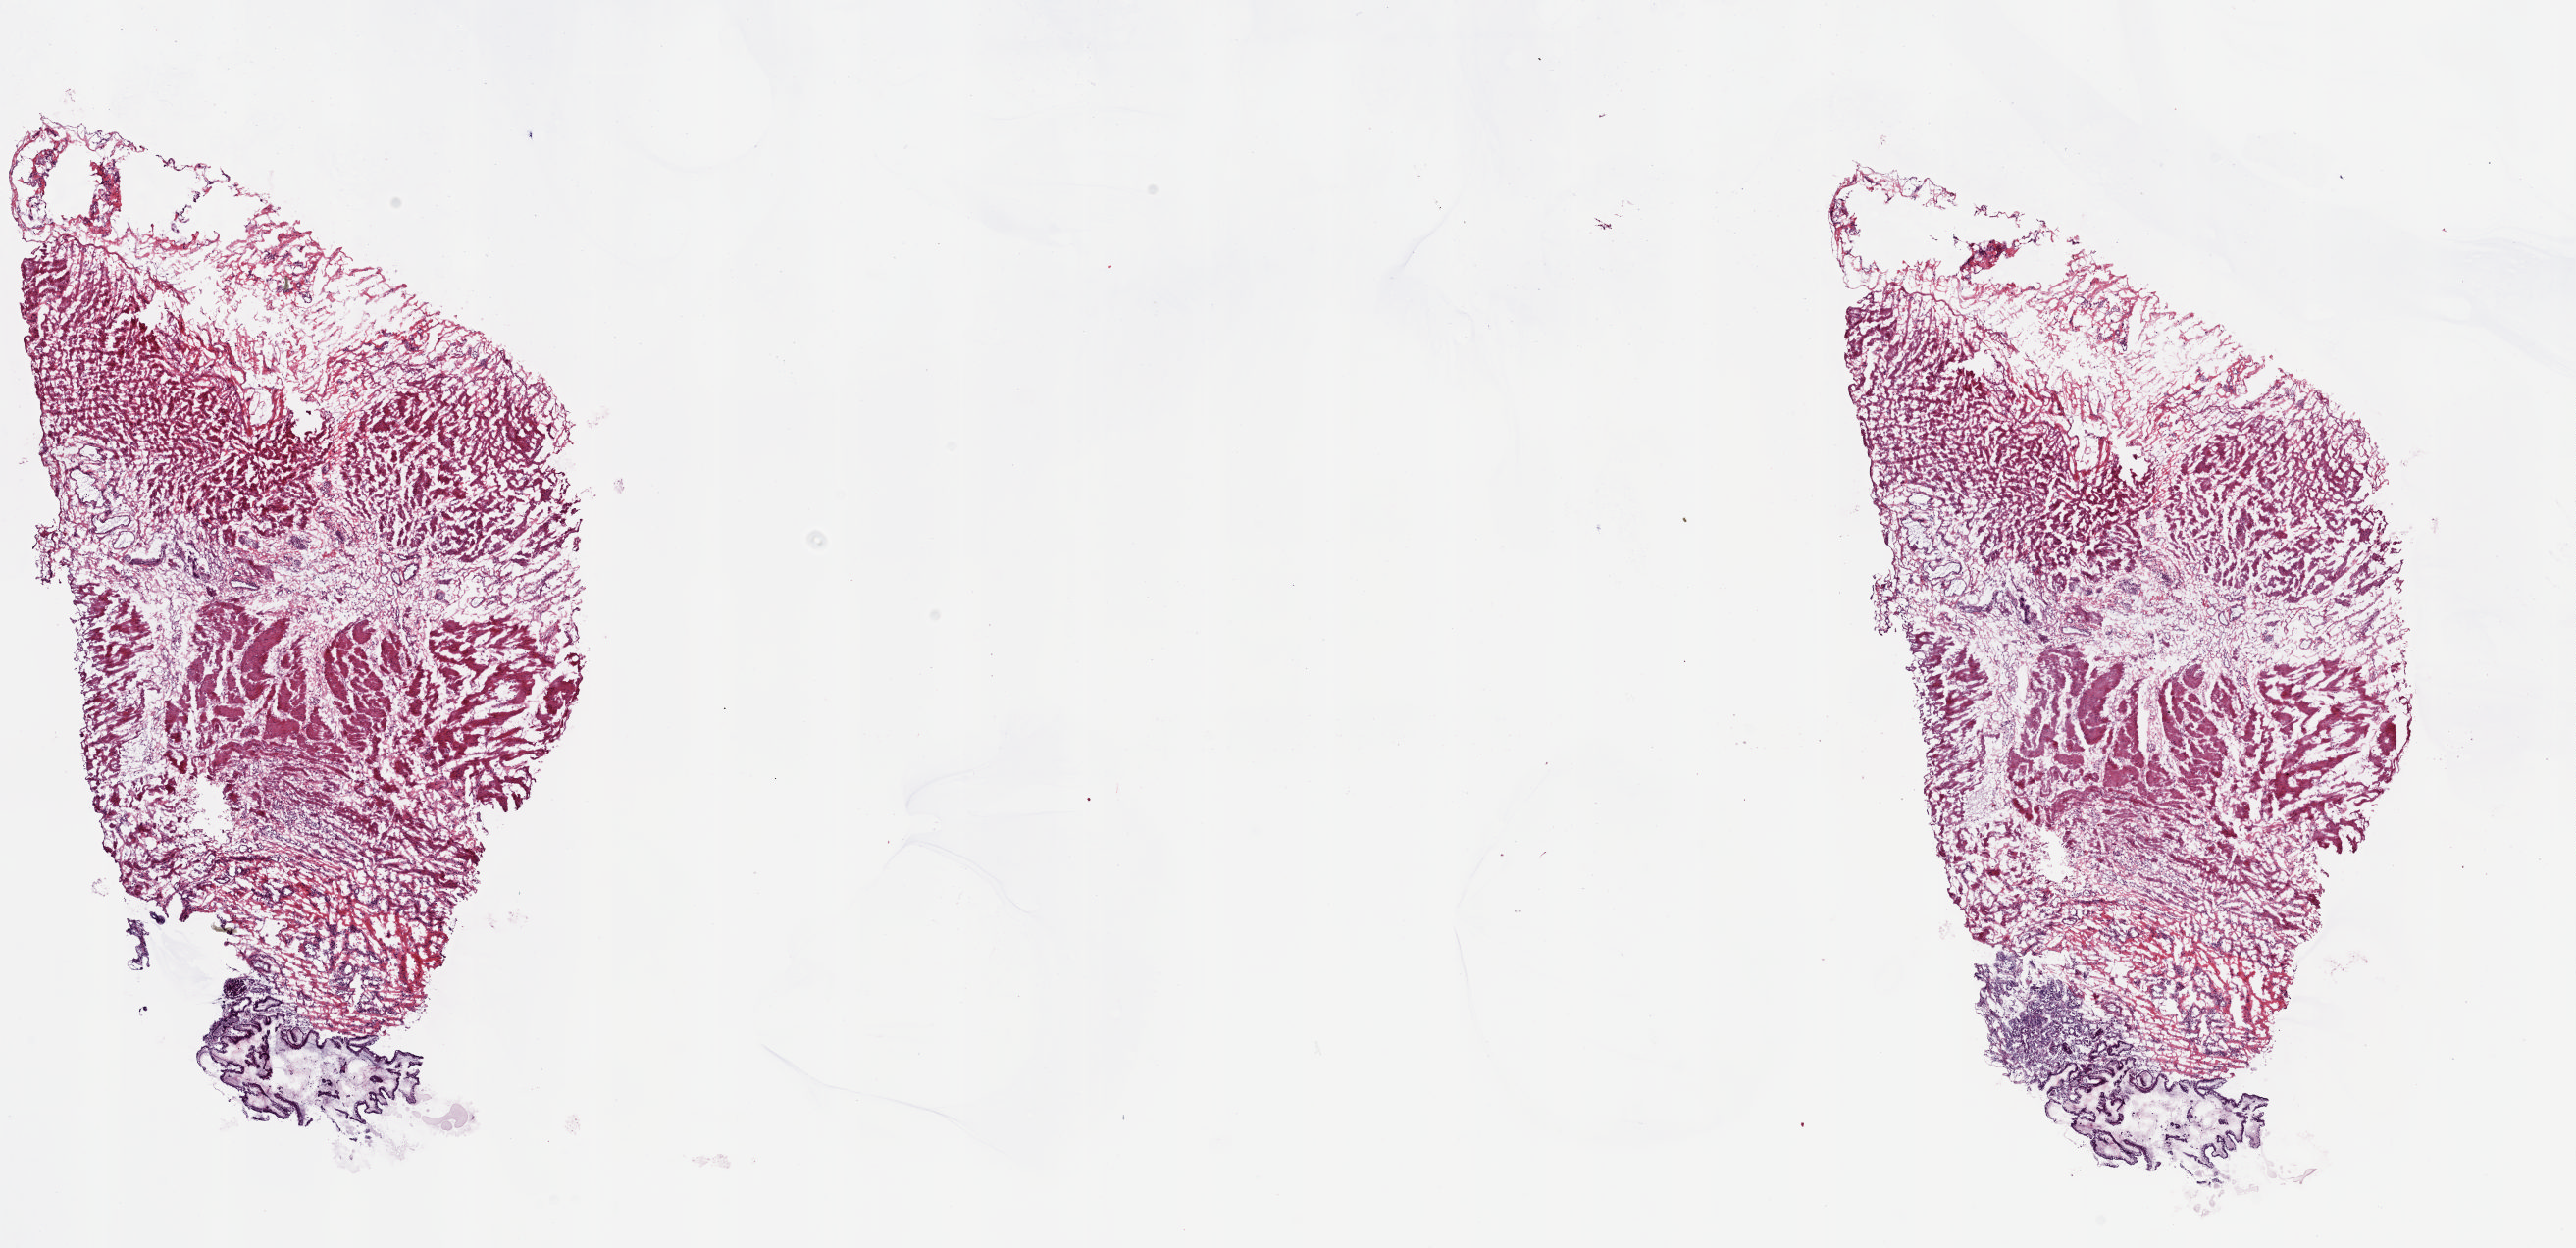
H&E whole-slide image, a low-resolution overview of the entire scanned area, about 20.8 x 10.1 mm (slide scanned at 20x); frozen section; sample: solid tissue normal (non-tumour tissue), esophagus. Male, age 75 years at initial diagnosis. Slide review estimates, as recorded: tumour cells 0%, tumour nuclei 0%, normal cells 100%, stromal cells 0%, necrosis 0%. Inflammatory infiltration, as recorded: lymphocyte infiltration 1%, monocyte infiltration 0%, neutrophil infiltration 0%.
* this section: solid tissue normal sample (biorepository sample class)
* patient diagnosis: Adenocarcinoma, NOS (lower third of esophagus)